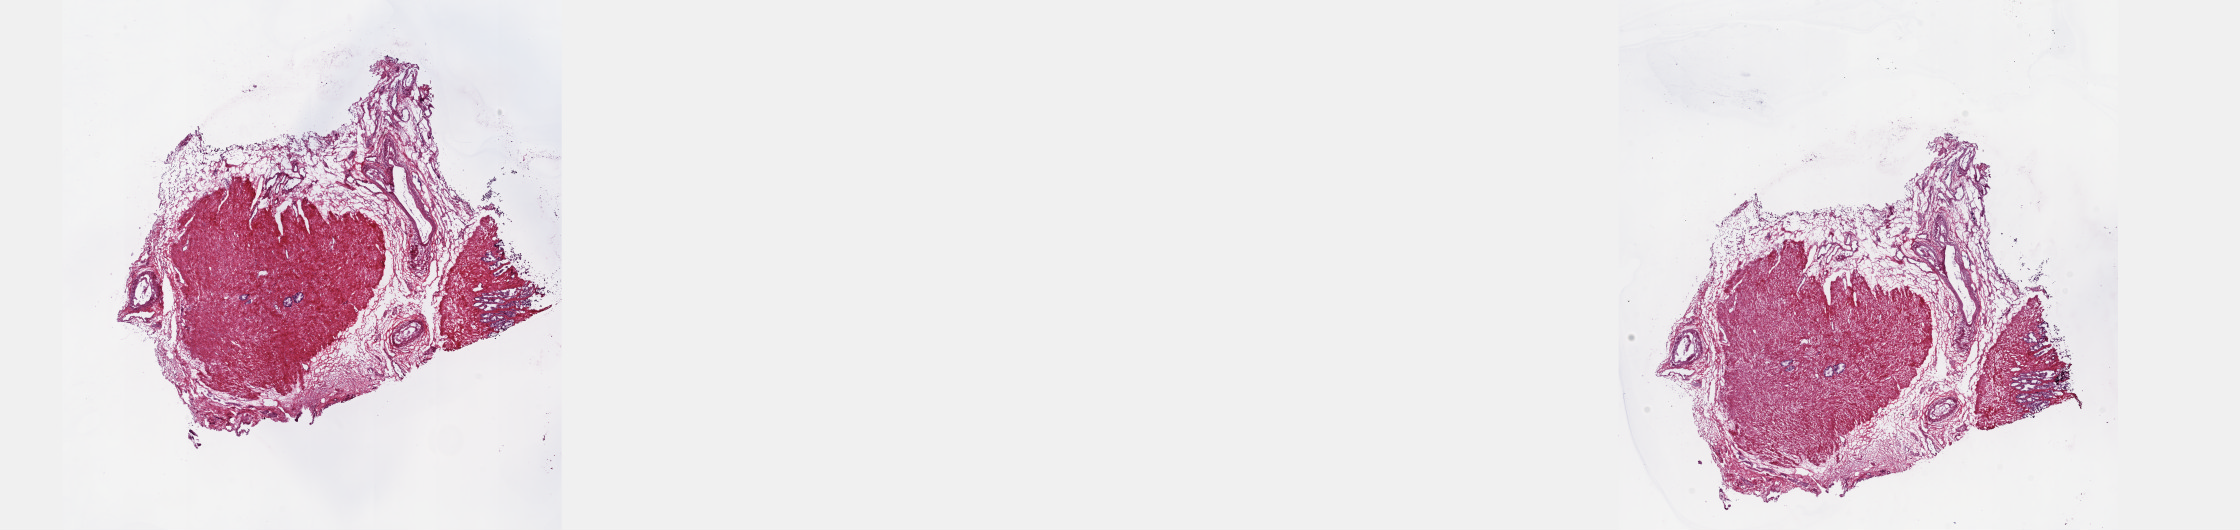
Whole-slide histology image, Hematoxylin and eosin (H&E) stained, a low-resolution overview of the entire scanned area, about 36.1 x 8.5 mm (from a 20x scan). Frozen section from the top of the tissue portion. Prostate, solid tissue normal (non-tumour tissue) sample. Male patient; age at initial diagnosis 57 years. Pathologist review of this section (percent, as recorded): tumour cells 0%, tumour nuclei 0%, normal cells 20%, stromal cells 80%, necrosis 0%. Infiltration values recorded for this section: lymphocyte infiltration 0%, monocyte infiltration 0%, neutrophil infiltration 0%.
* this section: solid tissue normal sample (biorepository sample class)
* patient diagnosis: Adenocarcinoma, NOS (prostate gland)